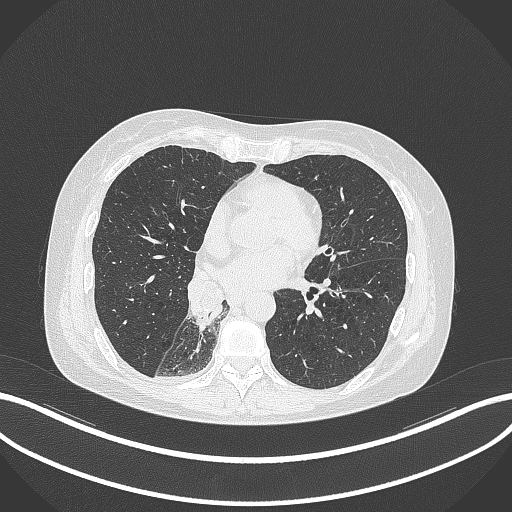
Chest CT, one axial slice. 120 kVp. Lung window (W 1500 / L -600 HU). 1 mm slice thickness. 512 × 512 image matrix. Patient: female, 63 years. Case-level facts recorded for this patient, not image findings: clinical TNM (as recorded): T1c N0 M0.
Annotated regions visible in this slice (bounding box drawn by a radiologist):
- lung tumour (recorded histology: adenocarcinoma): bounding box <187,265,226,332> (left, top, right, bottom; pixels)